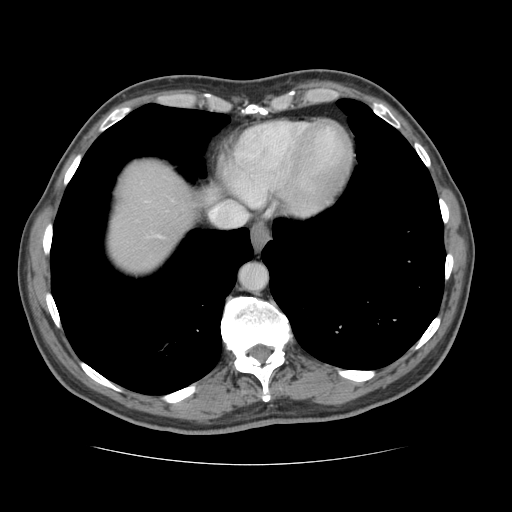
Contrast-enhanced abdominal CT, one axial slice; position 119 of 134 along the scan axis; 120 kVp; soft-tissue window (W 400 / L 40 HU); 512 × 512 image matrix, field of view 377 × 377 mm. Male patient, age 68 years. Case-level facts recorded for this patient, not image findings: diagnosis: colorectal cancer liver metastases, imaged before liver resection; multiple liver metastases: yes; largest metastasis: 2.2 cm.
Outlined on this slice (outlined manually by an expert reader):
- hepatic veins: bounding box (x1, y1, x2, y2) in pixels: (227, 204, 244, 214)
- liver: (108, 165, 199, 271)
- planned liver remnant (the part of the liver to remain after resection): (109, 164, 190, 271)